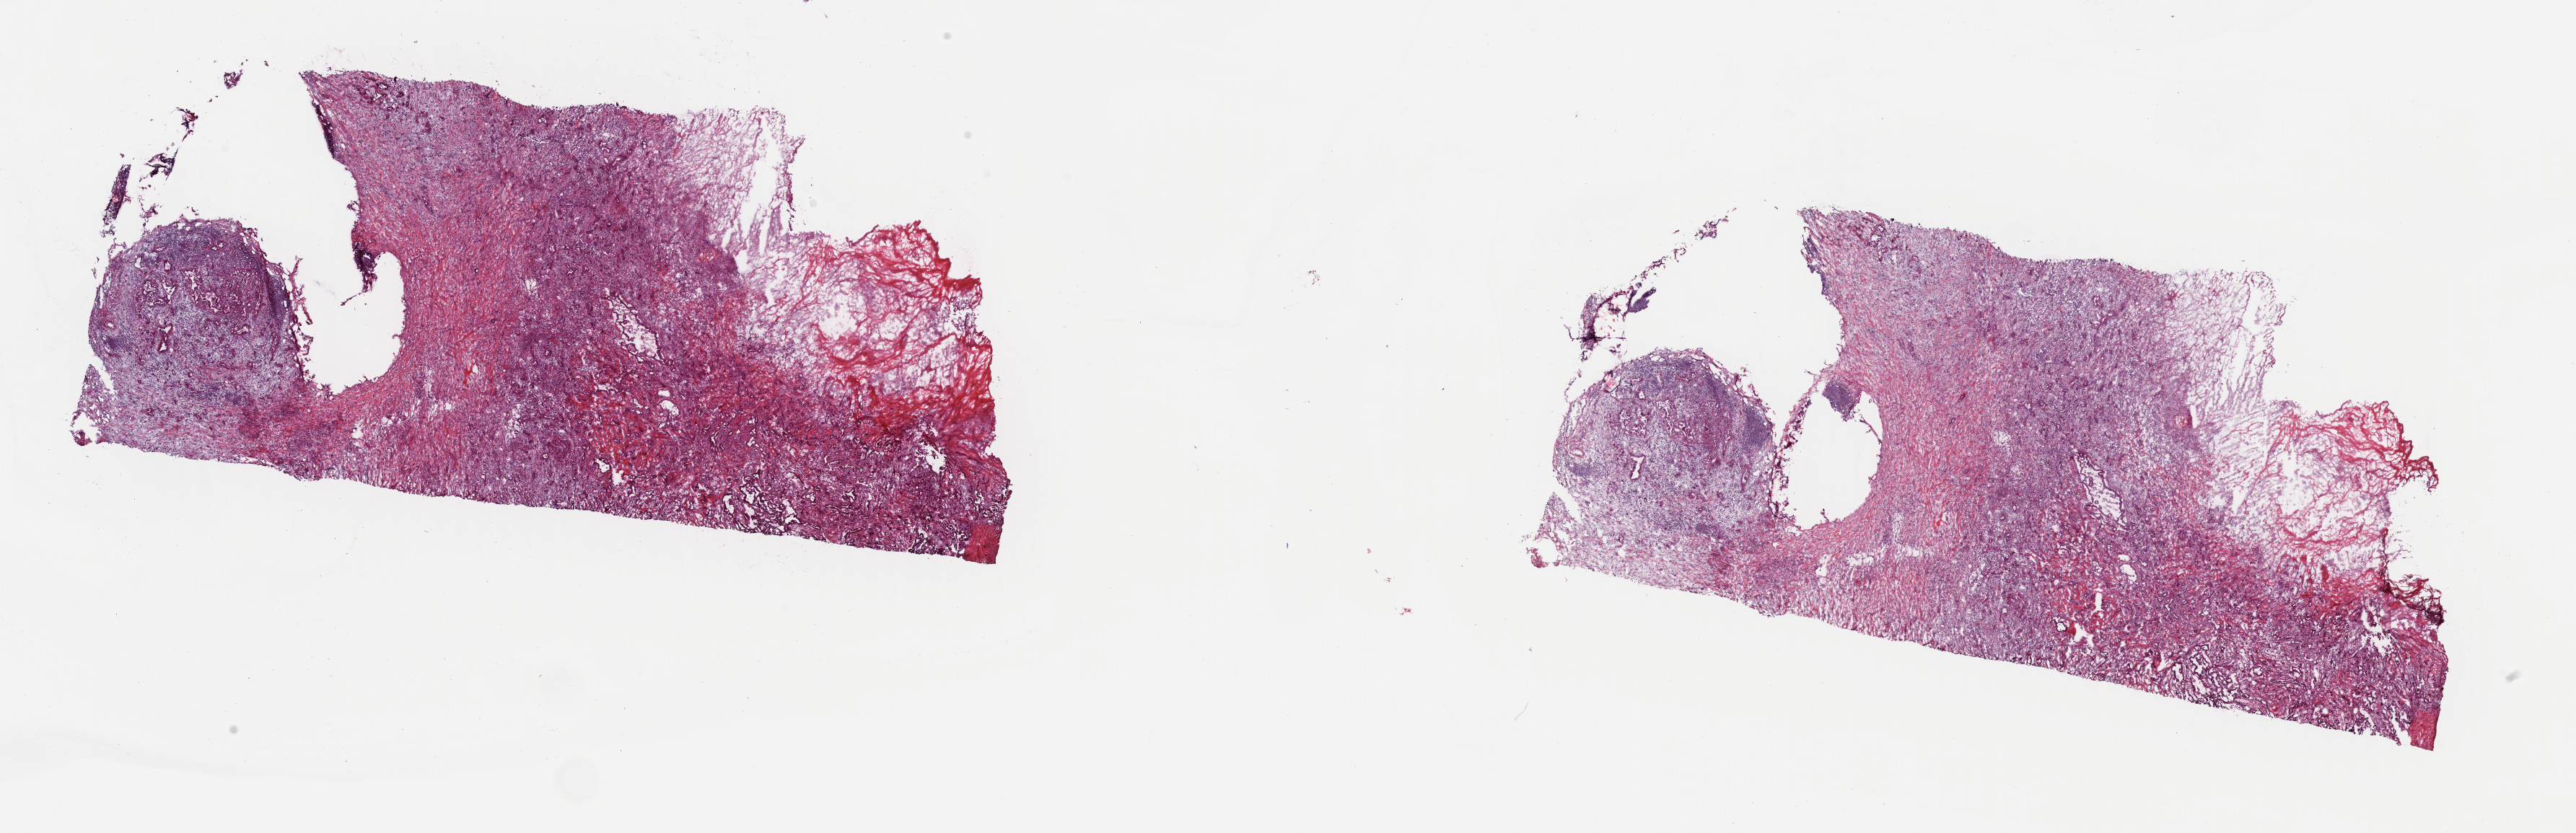
Digitized Hematoxylin and eosin (H&E) stained tissue section (whole slide) — whole scanned area (about 28.2 x 9.1 mm, slide scanned at 40x) shown as a low-resolution overview, frozen section, sample: primary tumour, pancreas. Female, age 64 years at initial diagnosis. Histologic grade: G3 (poorly differentiated). Composition of this section per pathologist review: tumour cells 30%, tumour nuclei 60%, normal cells 0%, stromal cells 55%, necrosis 15%. Inflammatory infiltration, as recorded: lymphocyte infiltration 12%, monocyte infiltration 1%, neutrophil infiltration 3%.
Pathologic diagnosis: Infiltrating duct carcinoma, NOS (head of pancreas). AJCC pathologic stage: IIB (7th edition).